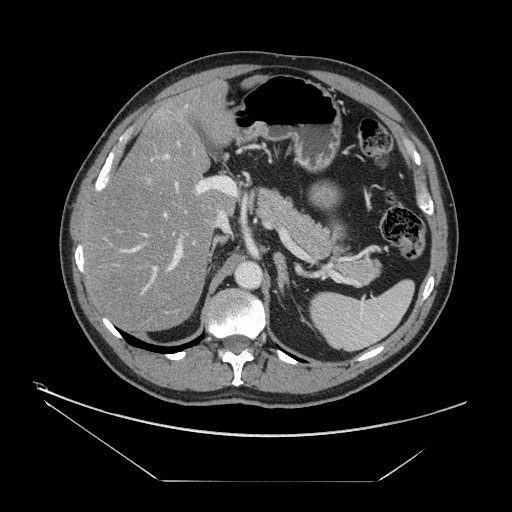
Contrast-enhanced abdominal CT, one axial slice; position 90 of 161 along the scan axis; 120 kVp; intravenous contrast given; soft-tissue window (W 400 / L 40 HU); 512 × 512 image matrix. Male patient, age 65 years. From the clinical record (not read from this slice): diagnosis: colorectal cancer liver metastases, imaged before liver resection; multiple liver metastases: yes; largest metastasis: 4.2 cm.
Structures marked on this image (manually delineated by an expert):
- hepatic veins: bounding box <116,179,179,294> (left, top, right, bottom; pixels)
- liver: <85,85,234,330>
- planned liver remnant (the part of the liver to remain after resection): <85,85,233,330>
- portal vein (with intrahepatic branches): <111,154,235,321>